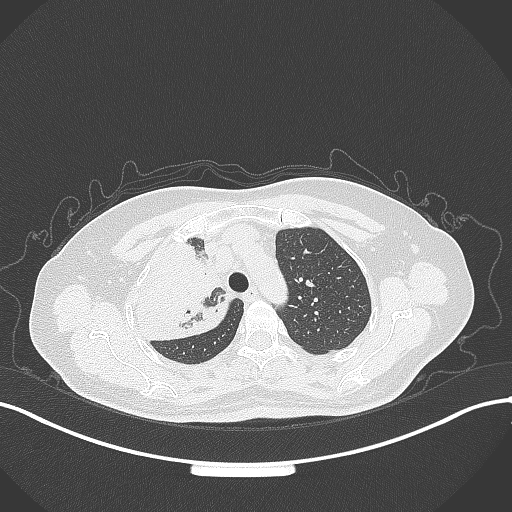
Chest CT, one axial slice; slice 244 of 309 in the series (ordered by position); reconstruction kernel B70f; lung window (W 1500 / L -600 HU); 512 × 512 image matrix, field of view 400 × 400 mm. Patient: female, 60 years. Case-level facts recorded for this patient, not image findings: clinical TNM (as recorded): T3 N1 M1.
Outlined on this slice (rectangle marked by the reading radiologist):
- lung tumour (recorded histology: adenocarcinoma): bounding box [x1, y1, x2, y2] px = [126, 236, 234, 347]